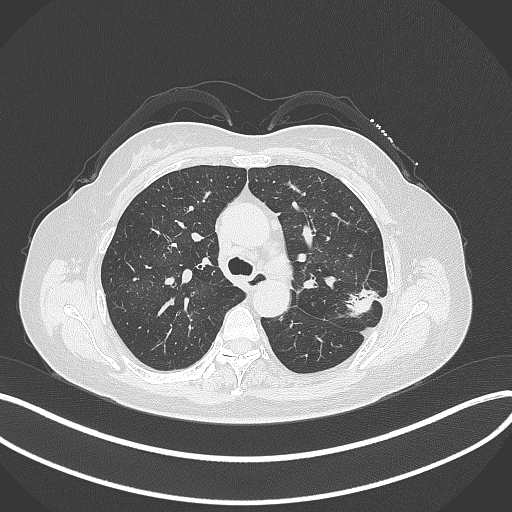
Chest CT, one axial slice. Slice 219 of 319 in the series (ordered by position). Reconstruction kernel B70f. 120 kVp. Lung window (W 1500 / L -600 HU). 512 × 512 image matrix. Female patient, age 60 years. From the clinical record (not read from this slice): clinical TNM (as recorded): T1c N0 M0.
Outlined on this slice (bounding box drawn by a radiologist):
- lung tumour (recorded histology: adenocarcinoma): bounding box <344,286,378,321> (left, top, right, bottom; pixels)